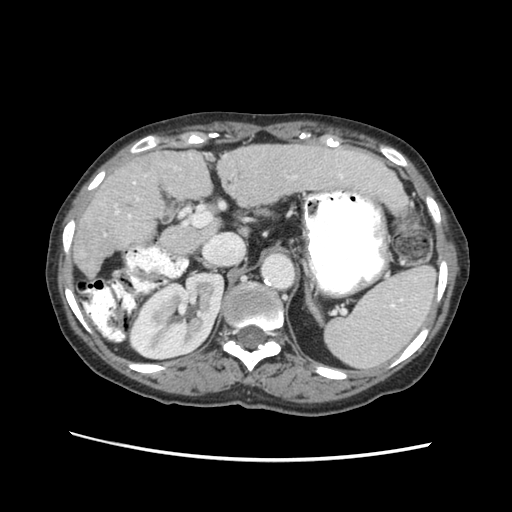
Contrast-enhanced abdominal CT (liver protocol), one axial slice; slice 33 of 63 in the series (ordered by position); reconstruction kernel STANDARD; 120 kVp; soft-tissue window (W 400 / L 40 HU); 512 × 512 image matrix, field of view 340 × 340 mm. Case-level facts recorded for this patient, not image findings: diagnosis: hepatocellular carcinoma (patient treated with transarterial chemoembolisation; whether this scan precedes or follows treatment is not stated here); TNM stage (as recorded): Stage-I; Child-Pugh class: B; tumour nodularity: uninodular.
Outlined on this slice (semi-automatic segmentation, software-assisted and operator-edited):
- abdominal aorta: bounding box (x1, y1, x2, y2) in pixels: (264, 254, 292, 286)
- liver parenchyma outside the tumour (the mass and vessels are separate outlines, so this box may not span the whole liver): (74, 140, 406, 276)
- liver vessels: (103, 165, 343, 235)